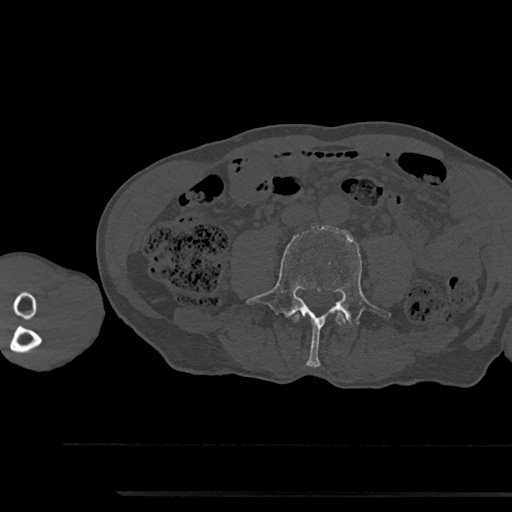
CT including the spine, one axial slice. Position 425 of 797 along the scan axis. Bone window (W 1800 / L 400 HU). 0.5 mm slice thickness. 512 × 512 image matrix, field of view 367 × 367 mm. Patient: male, 79 years. From the clinical record (not read from this slice): primary cancer: prostate.
Structures marked on this image (semi-automatic segmentation, software-assisted and operator-edited):
- L3 vertebra: bounding box <294,313,345,324> (left, top, right, bottom; pixels)
- L4 vertebra: <246,225,391,367>